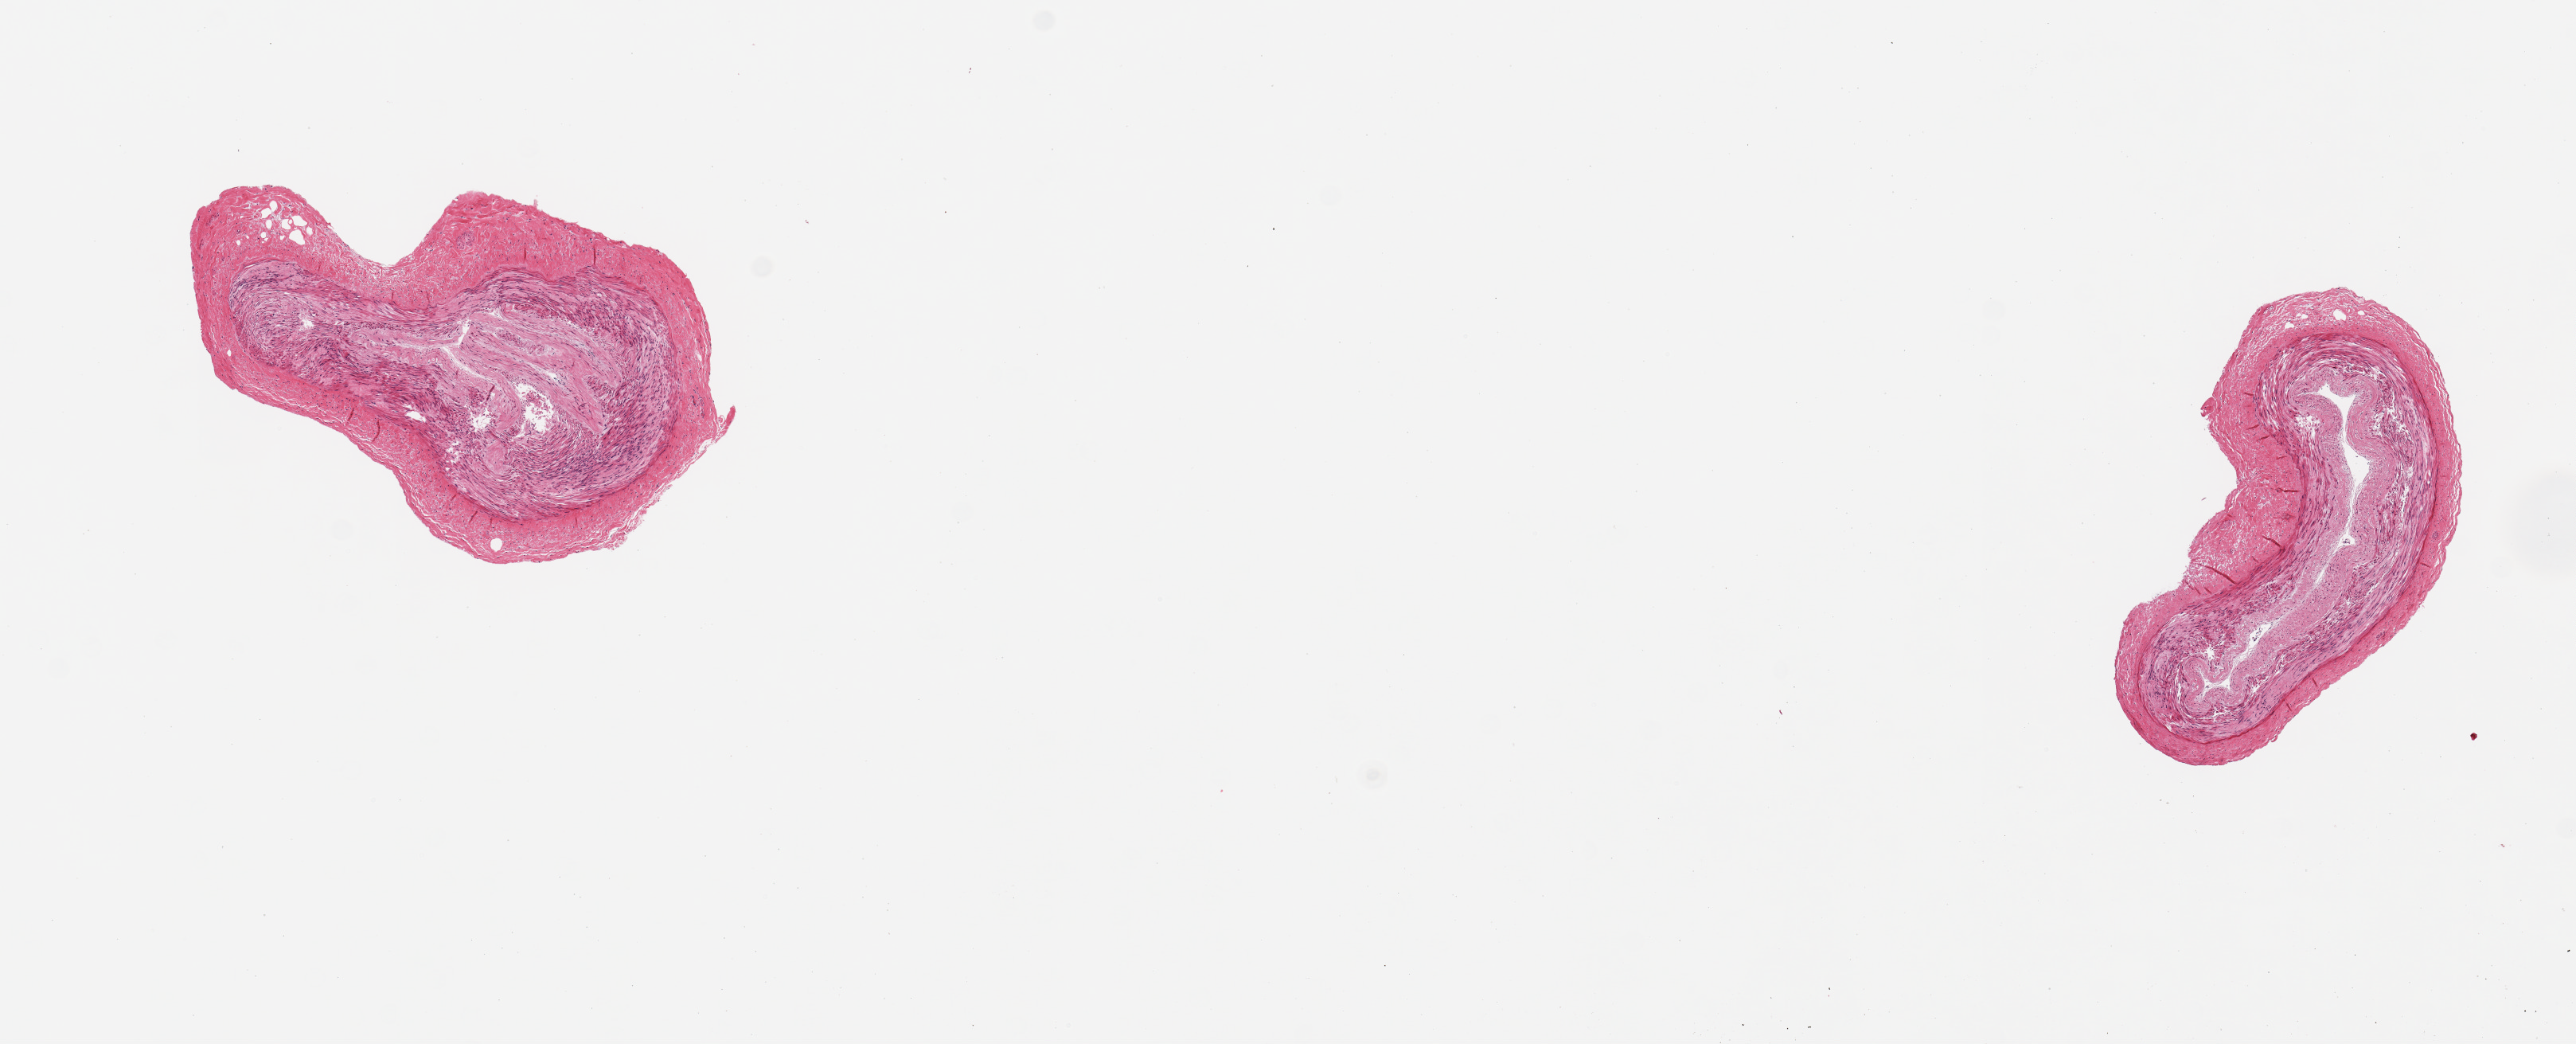
Digitized hematoxylin and eosin (H&E)-stained section, brightfield — shown as a low-resolution overview of the whole scanned area (about 12.8 x 5.2 mm), PAXgene-fixed, paraffin-embedded tissue, sampled site (target tissue): tibial artery, tissue donor sample. Donor sex: female.
Pathologist's review note for this sample: 2 pieces; well trimmed; no plaques; thick fibrous adventitia (up to 0.3mm).